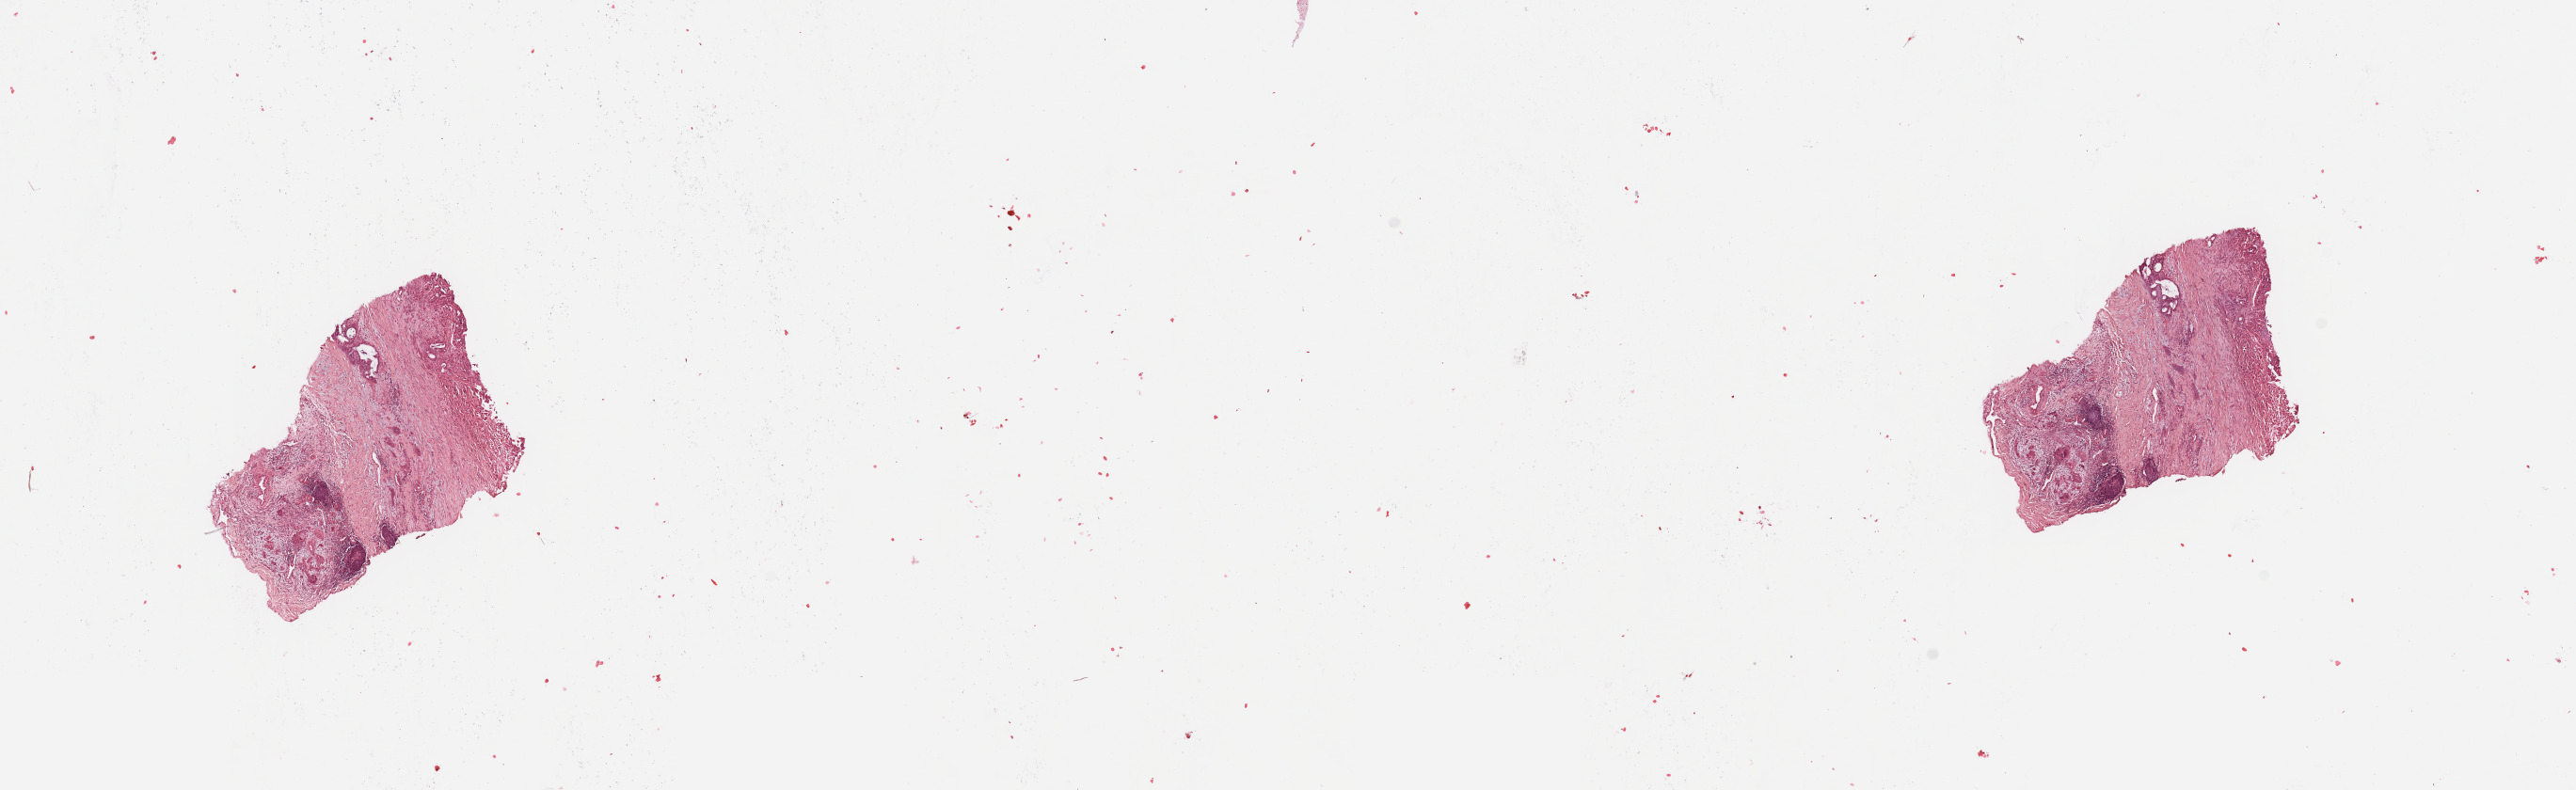
Whole-slide histology image, H&E — whole scanned area (about 21.7 x 6.6 mm) shown as a low-resolution overview, tumour tissue sample, sampled site: pancreas. Male, 68 y/o. Histologic grade: G3 (poorly differentiated). Slide review estimates, as recorded: tumour nuclei 25%, necrosis 2%.
• AJCC pathologic stage: IIA
• primary tumour site (as recorded): head
• histologic diagnosis: Infiltrating duct carcinoma, NOS